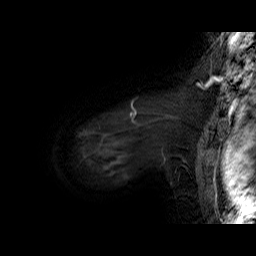
Breast MRI (dynamic contrast-enhanced), one sagittal slice; position 57 of 60 along the scan axis; dynamic contrast-enhanced series, time point 2 of 6 at this slice position (early post-contrast); 1.5 T; TE 6.3 ms, TR 32.9 ms; 4 mm slice thickness; 256 × 256 image matrix, field of view 200 × 200 mm. Female patient. From the clinical record (not read from this slice): setting: breast cancer imaged before/during neoadjuvant chemotherapy; receptor status: HER2-positive.
Structures marked on this image (semi-automatically segmented with operator editing):
- analysis volume of interest (the breast-tissue region the enhancement analysis was run in; not a lesion): box from (x=81, y=92) to (x=195, y=174) px
- tumour enhancement mask (voxels above the 100 % enhancement threshold inside the analysis volume of interest): (x=130, y=106)–(x=137, y=121)